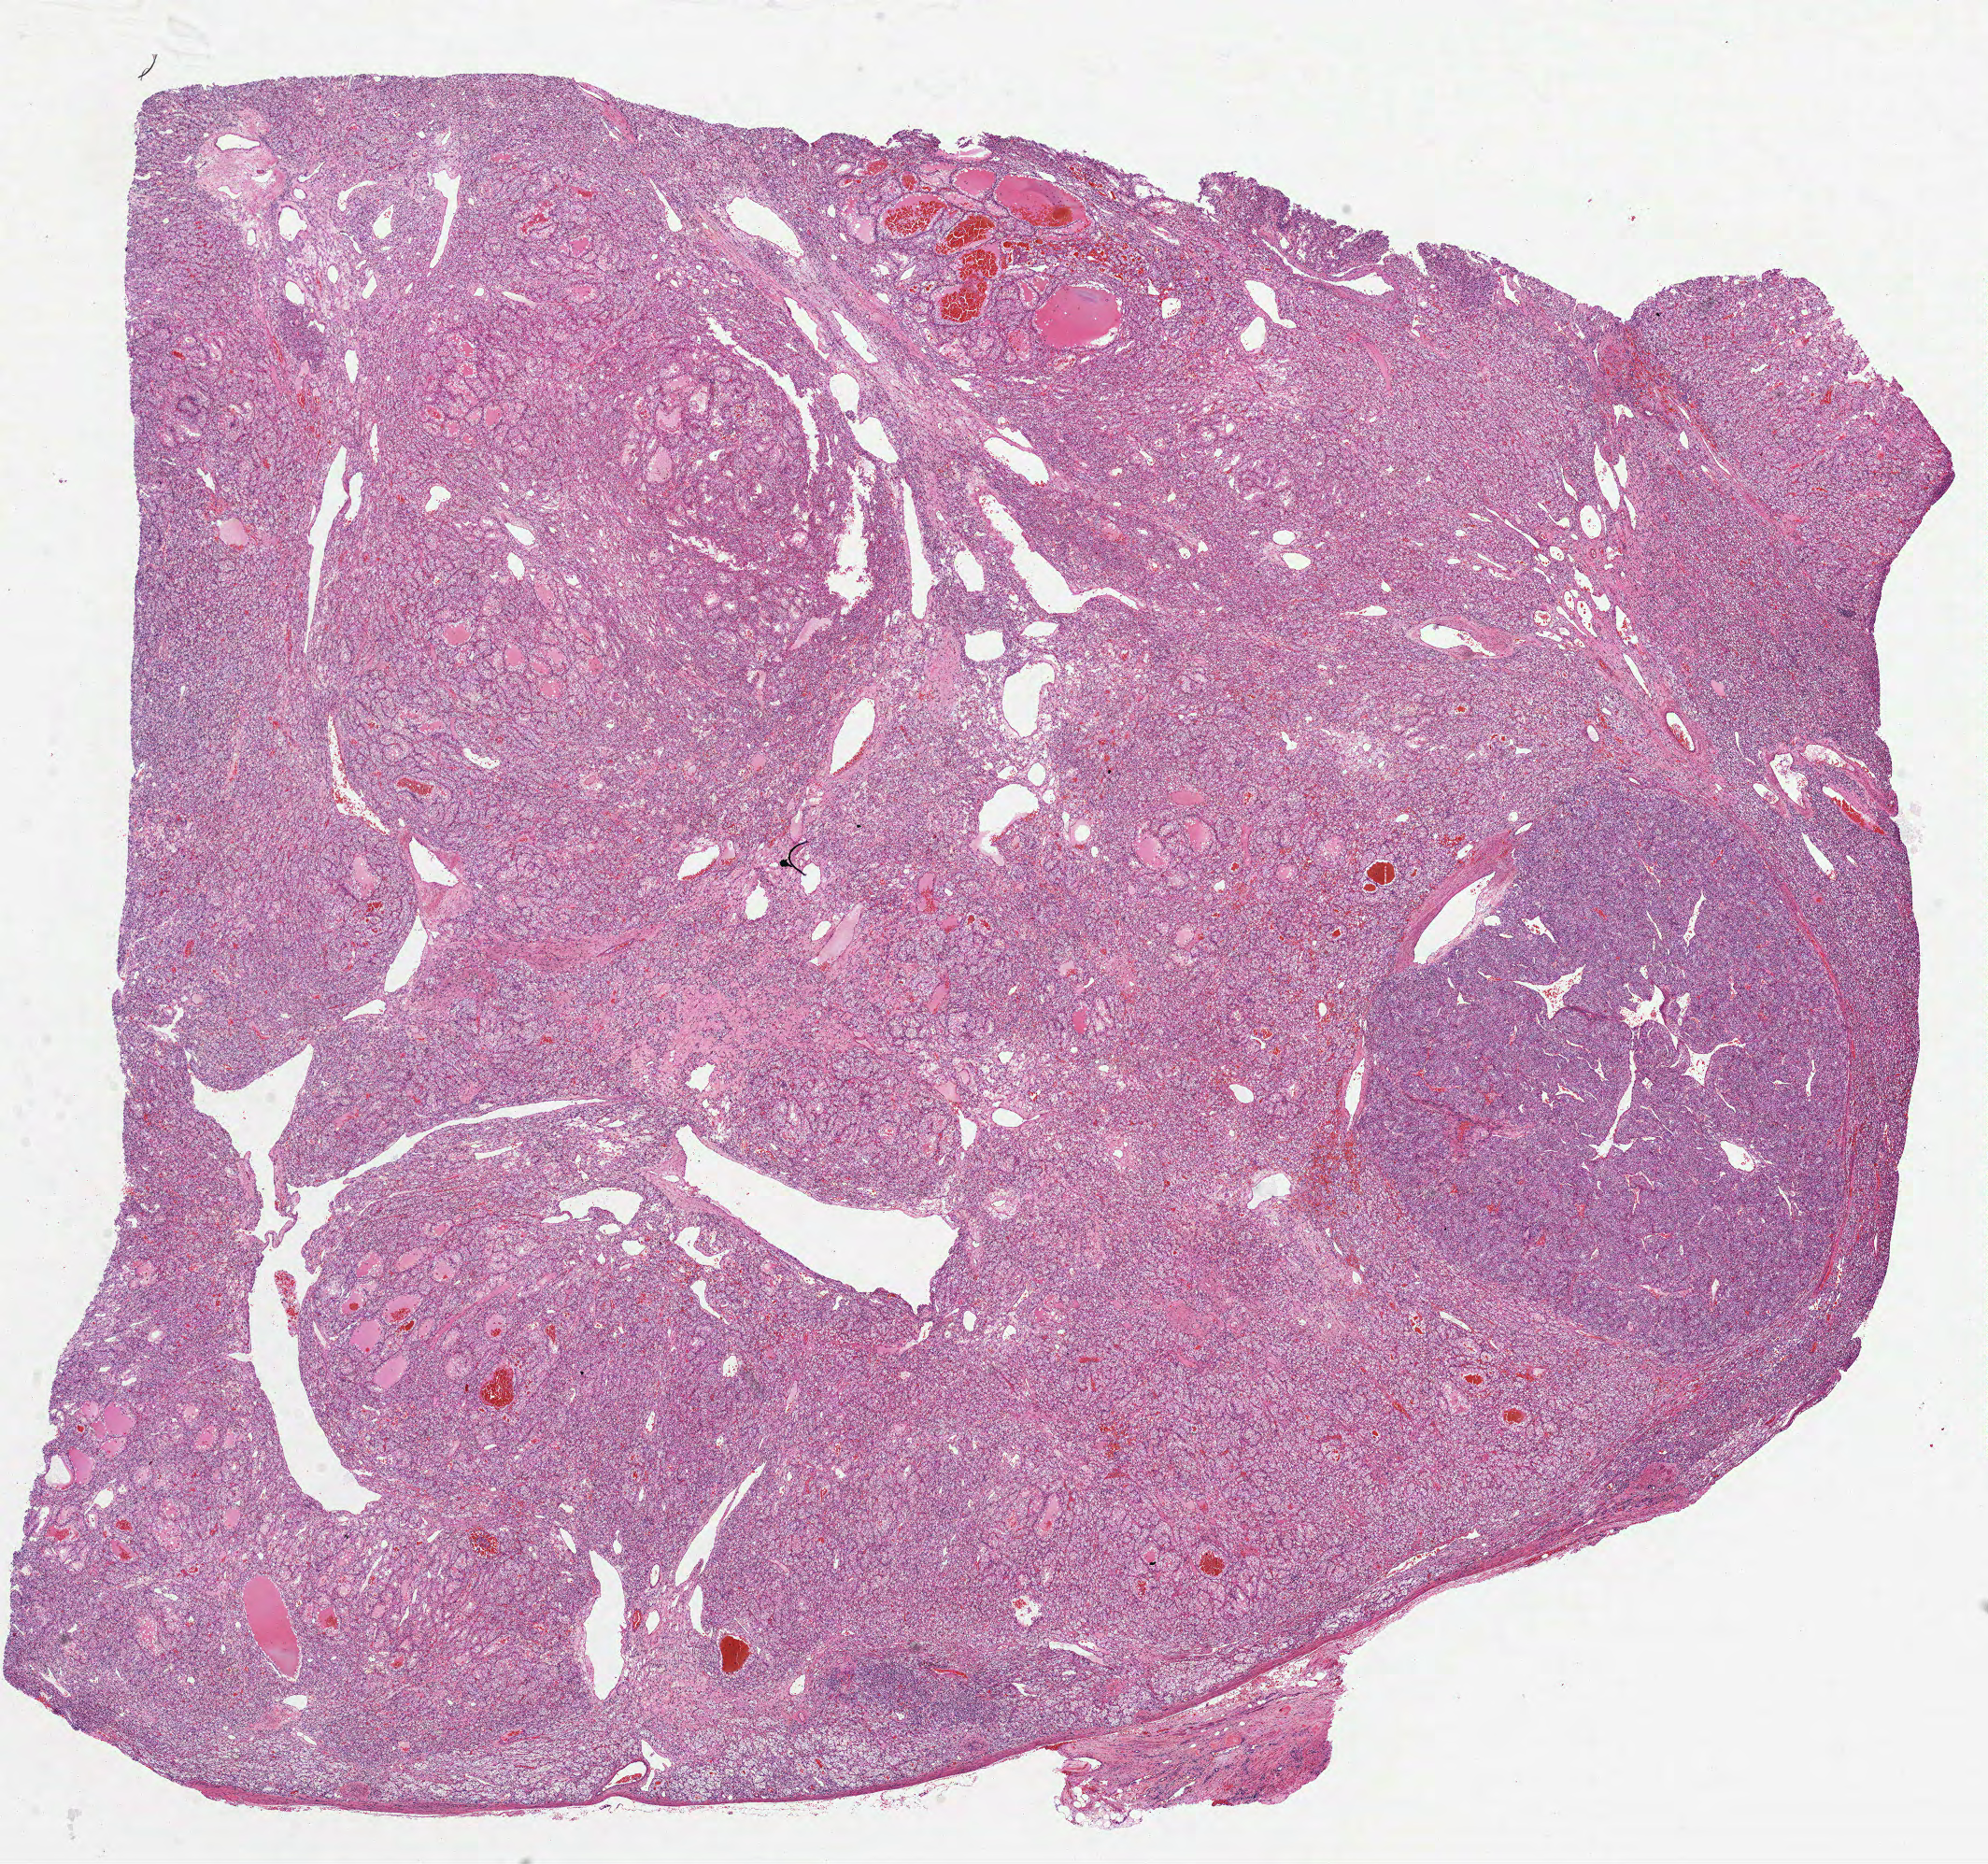
Hematoxylin and eosin (H&E) stained whole-slide image, a low-resolution overview of the entire scanned area, about 17.2 x 16.1 mm (slide scanned at 40x); FFPE section; kidney, primary tumour sample. Female, age 61 years at initial diagnosis.
Histologic diagnosis: Clear cell adenocarcinoma, NOS.